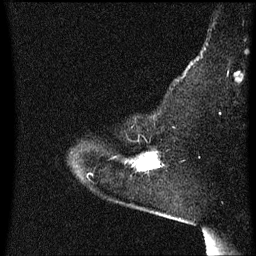
Breast MRI (dynamic contrast-enhanced), one sagittal slice; slice 48 of 60 in the series (ordered by position); dynamic contrast-enhanced series, image 2 of 3 at this slice position (ordered by acquisition); 1.5 T; TE 4.2 ms, TR 8.4 ms; 2 mm slice thickness; 256 × 256 image matrix. Female patient, age 54 years. Case-level facts recorded for this patient, not image findings: setting: breast cancer imaged before/during neoadjuvant chemotherapy; receptor status: HR-positive, HER2-negative.
Outlined on this slice (semi-automatic segmentation, software-assisted and operator-edited):
- analysis volume of interest (the breast-tissue region the enhancement analysis was run in; not a lesion): bounding box [x1, y1, x2, y2] px = [131, 154, 162, 171]
- tumour enhancement mask (voxels above the 70 % enhancement threshold inside the analysis volume of interest): [135, 154, 160, 171]